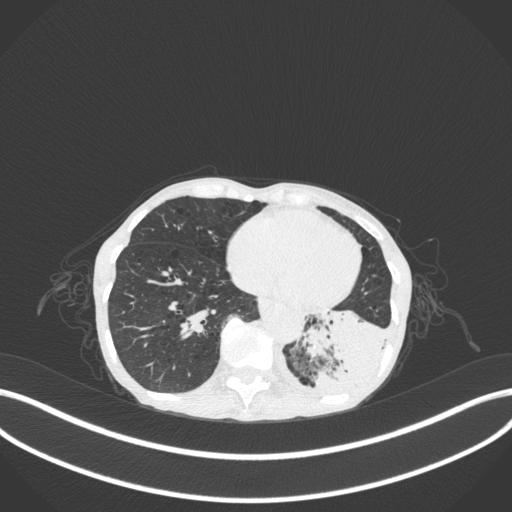
Chest CT, one axial slice. Slice 69 of 347 in the series (ordered by position). Reconstruction kernel B31f. 120 kVp. Lung window (W 1500 / L -600 HU). 1 mm slice thickness. 512 × 512 image matrix, field of view 400 × 400 mm. Female patient, age 70 years. Case-level facts recorded for this patient, not image findings: clinical TNM (as recorded): T3 N0 M0; histopathological grade: G3.
Annotated regions visible in this slice (rectangle marked by the reading radiologist):
- lung tumour (recorded histology: small cell carcinoma): bounding box [x1, y1, x2, y2] px = [296, 303, 388, 405]